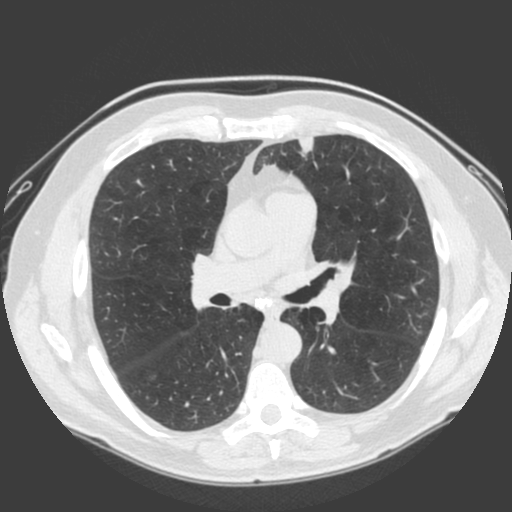
Low-dose screening chest CT, one axial slice; position 105 of 185 along the scan axis; 120 kVp; lung window (W 1500 / L -600 HU); 2 mm slice thickness; 512 × 512 image matrix, field of view 360 × 360 mm.
Structures marked on this image (manually delineated by an expert):
- lesion 1 (tumor, lower lobe of left lung): bounding box [x1, y1, x2, y2] px = [298, 137, 314, 157]